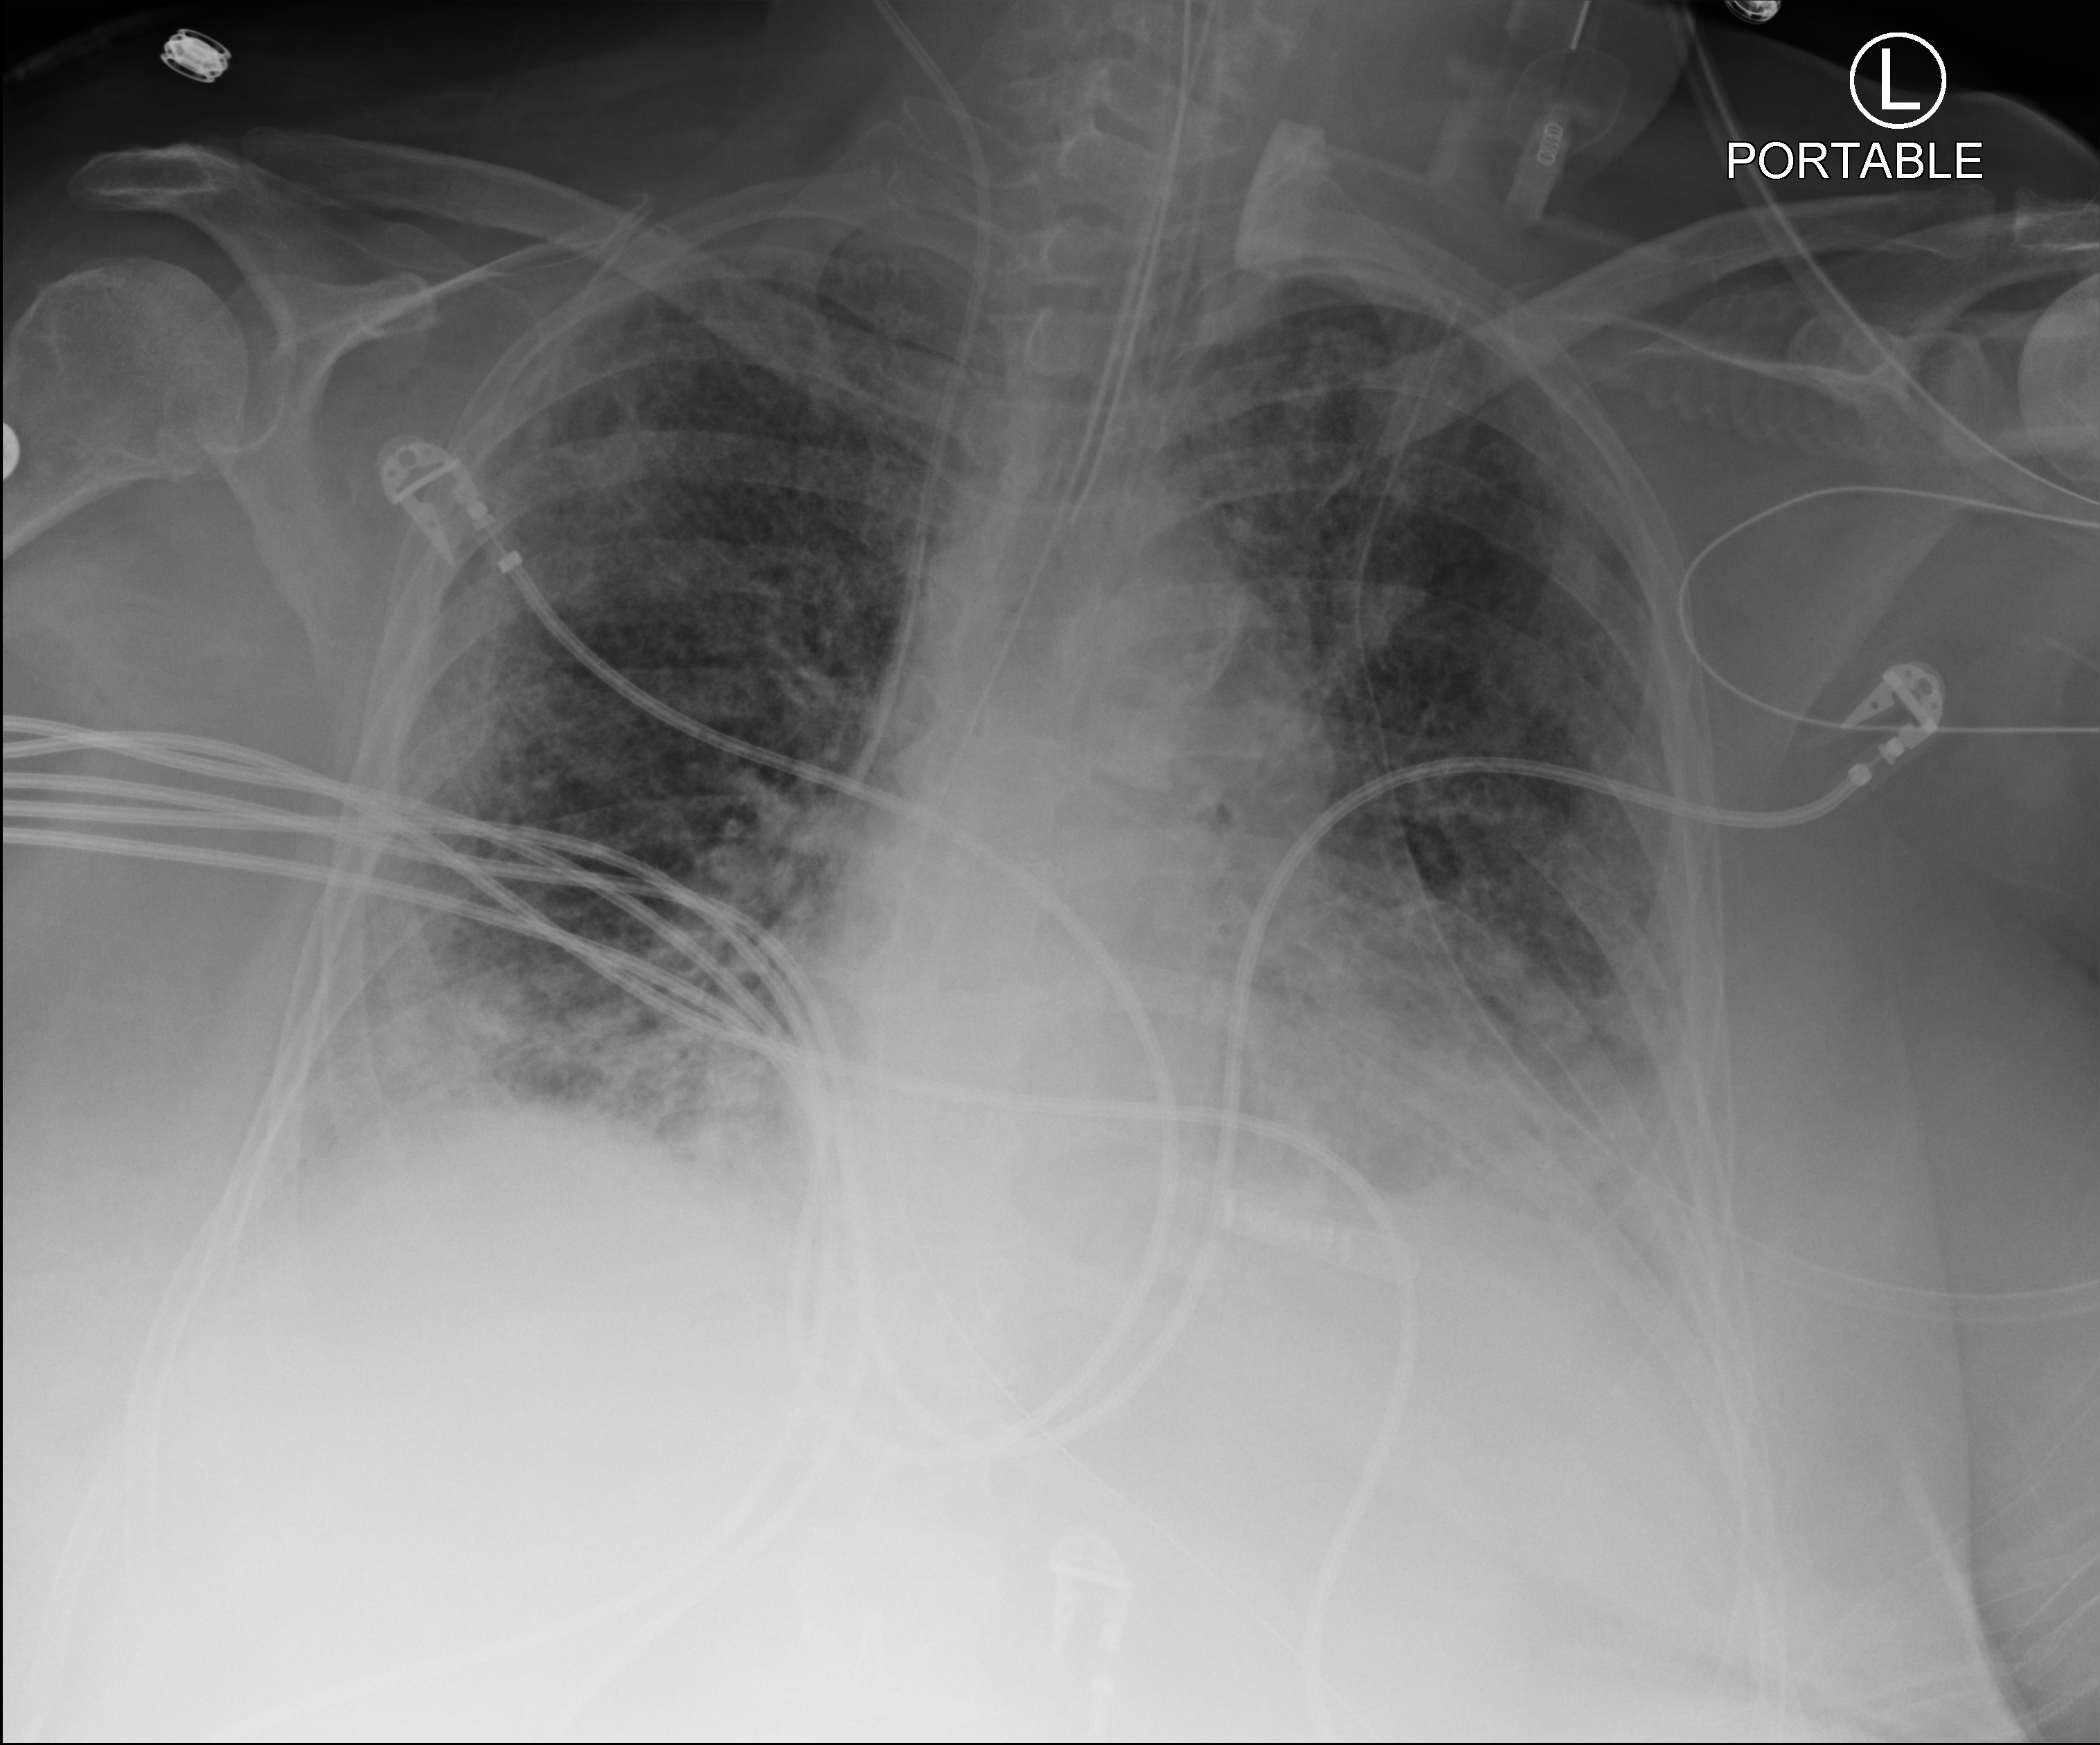
Portable chest radiograph; anteroposterior (AP) projection. Female patient hospitalised with COVID-19, age 60–74 years.
Admission-level facts for this patient (not findings on this image; timing relative to this image not recorded):
- other chronic lung disease (admission record): yes
- diabetes (admission record): yes
- admitted to intensive care during this hospital stay: yes